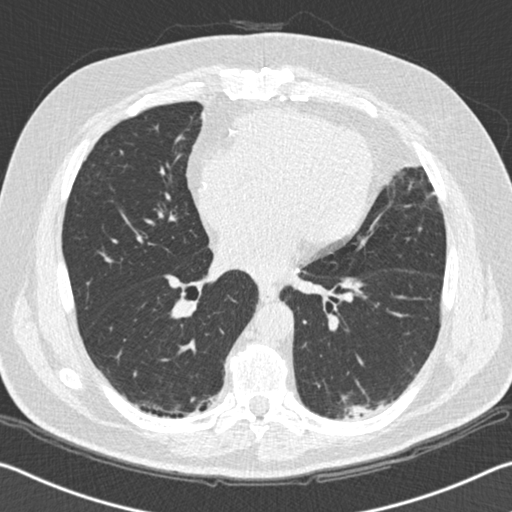
Chest CT (low-dose screening protocol), one axial image; second screening round (one year after baseline); lung window (W 1500 / L -600 HU); slice 90 of 172 in the series. Male participant, aged 65 years at enrolment. Former smoker at enrolment.
Expert reader's lesion annotation, bounding box (x1, y1, x2, y2) in pixels: (325, 390, 394, 434). Reader record for this screening exam (exam-level; its link to the box is not recorded): non-calcified nodule or mass ≥4 mm, left lower lobe, 19 × 11 mm, spiculated (stellate) margins, soft tissue attenuation, pre-existing on the prior screen: yes; interval growth: yes. Official screen result: positive, change unspecified: nodule(s) >= 4 mm or enlarging nodule(s), mass(es), or other non-specific abnormalities suspicious for lung cancer.